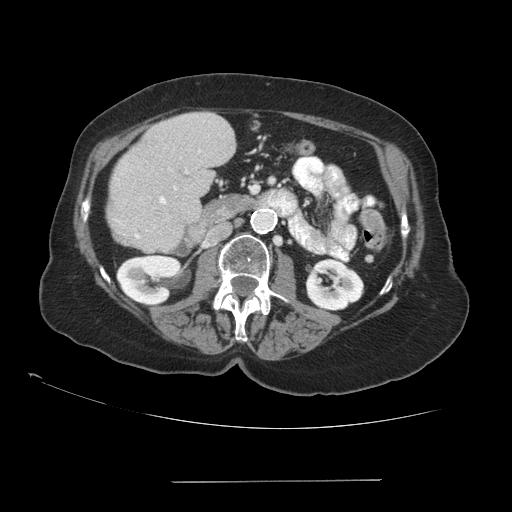
Contrast-enhanced abdominal CT (liver protocol), one axial slice; slice 34 of 89 in the series (ordered by position); soft-tissue window (W 400 / L 40 HU); 2.5 mm slice thickness; 512 × 512 image matrix, field of view 400 × 400 mm. From the clinical record (not read from this slice): diagnosis: hepatocellular carcinoma (patient treated with transarterial chemoembolisation; whether this scan precedes or follows treatment is not stated here); TNM stage (as recorded): Stage-IVA; Child-Pugh class: A; tumour nodularity: uninodular.
Outlined on this slice (semi-automatically segmented with operator editing):
- liver parenchyma outside the tumour (the mass and vessels are separate outlines, so this box may not span the whole liver): box from (x=107, y=112) to (x=234, y=252) px
- liver vessels: (x=135, y=150)–(x=201, y=239)